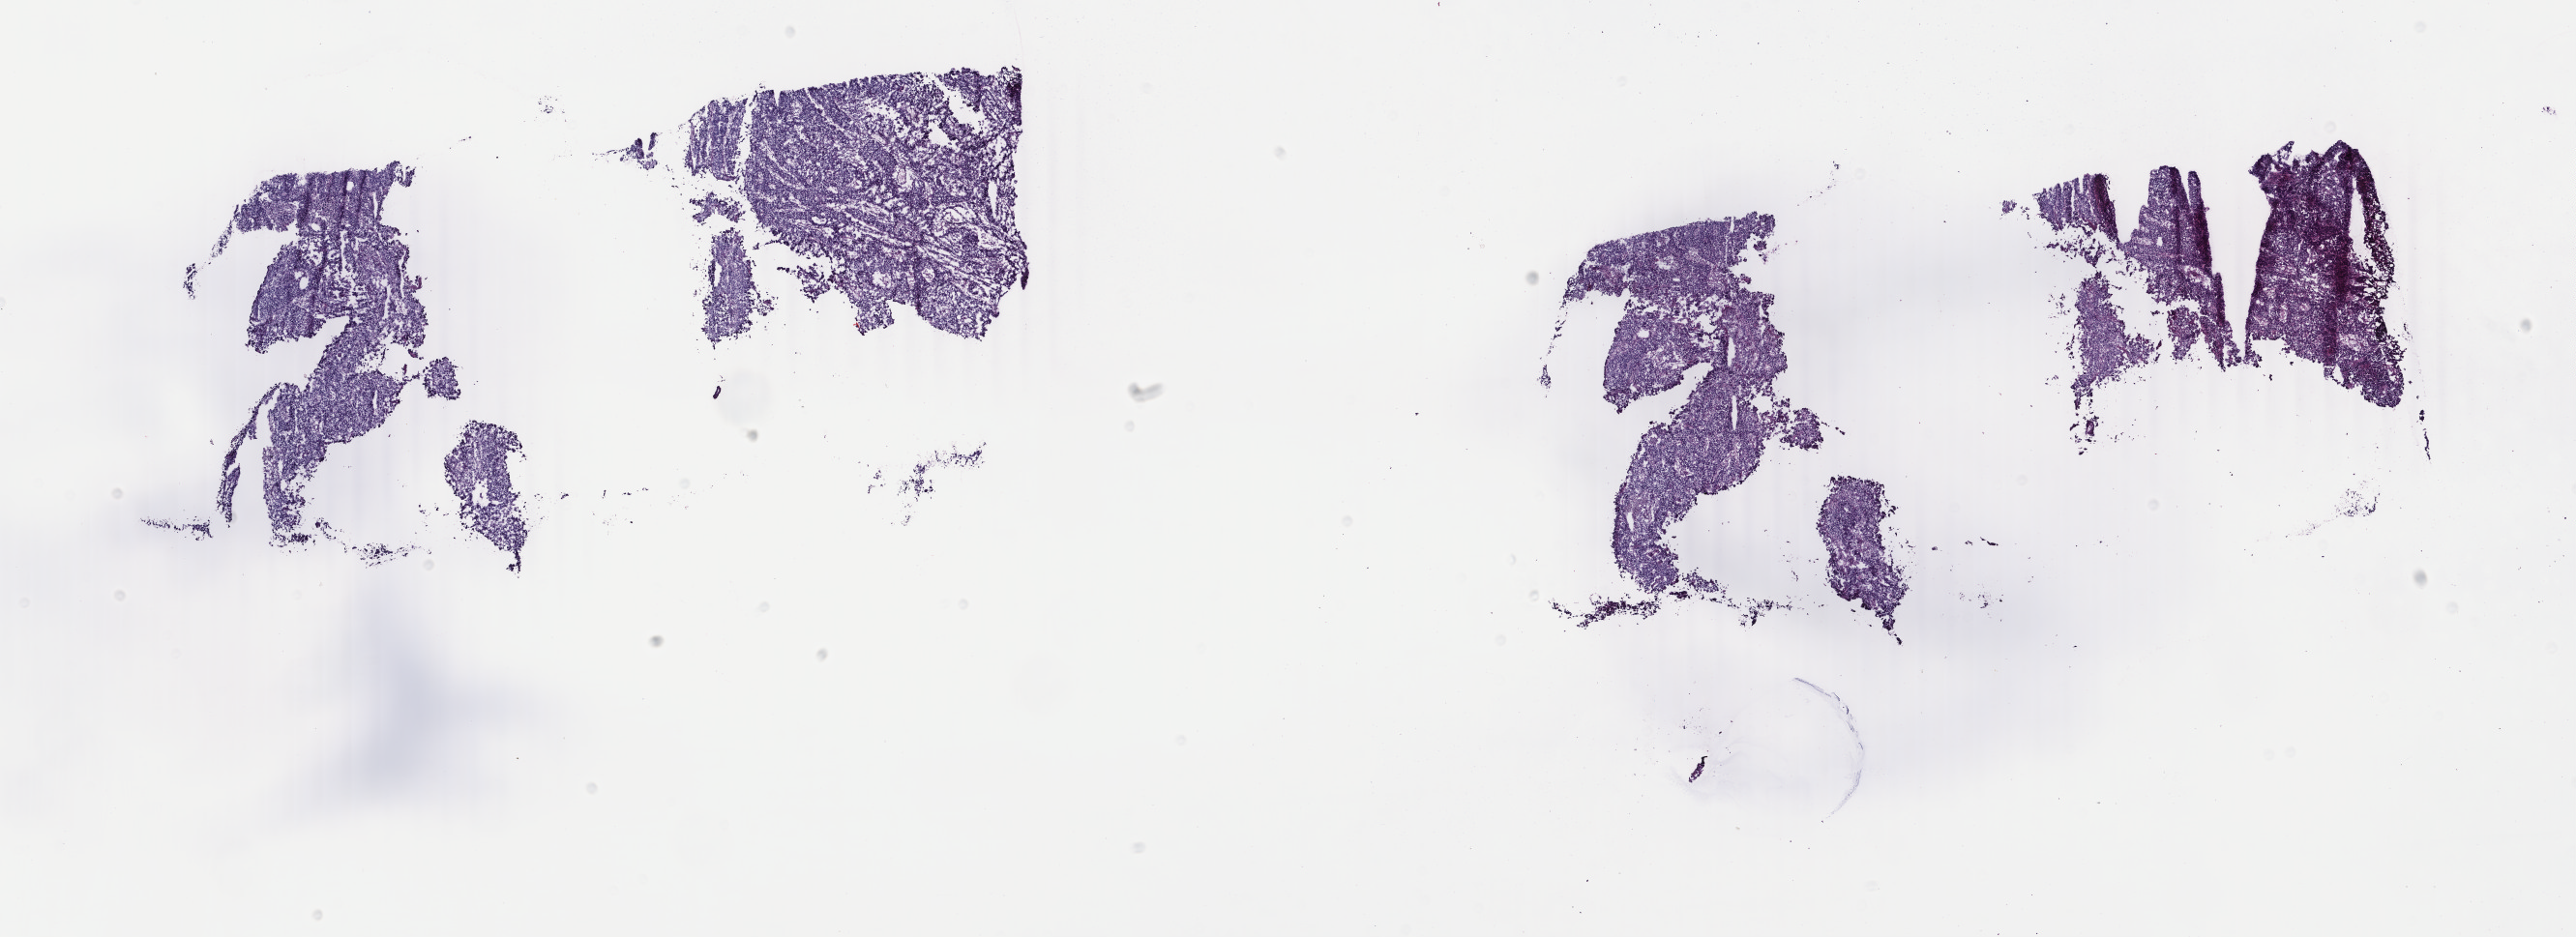
Digitized Hematoxylin and eosin (H&E) stained tissue section (whole slide), a low-resolution overview of the entire scanned area, about 21.2 x 7.7 mm (acquisition: 40x scan); frozen section from the top of the tissue portion; uterus, primary tumour sample. Female patient; age at initial diagnosis 62 years. Composition of this section per pathologist review: tumour cells 90%, tumour nuclei 90%.
Pathologic diagnosis: Endometrioid adenocarcinoma, NOS (endometrium).